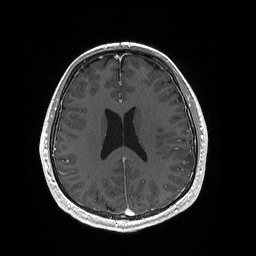
Brain MRI from a brain-tumour surgery series, one axial slice. Slice 84 of 192 in the series (ordered by position). T1-weighted post-contrast. 1 mm slice thickness. 256 × 256 image matrix. From the clinical record (not read from this slice): histopathology: Dysembryoplastic neuroepithelial tumor; WHO grade: 1; IDH mutation: no; tumour location: Left Inferior Parietal.
Structures marked on this image (expert manual segmentation):
- tumour: bounding box (x1, y1, x2, y2) in pixels: (180, 159, 190, 166)